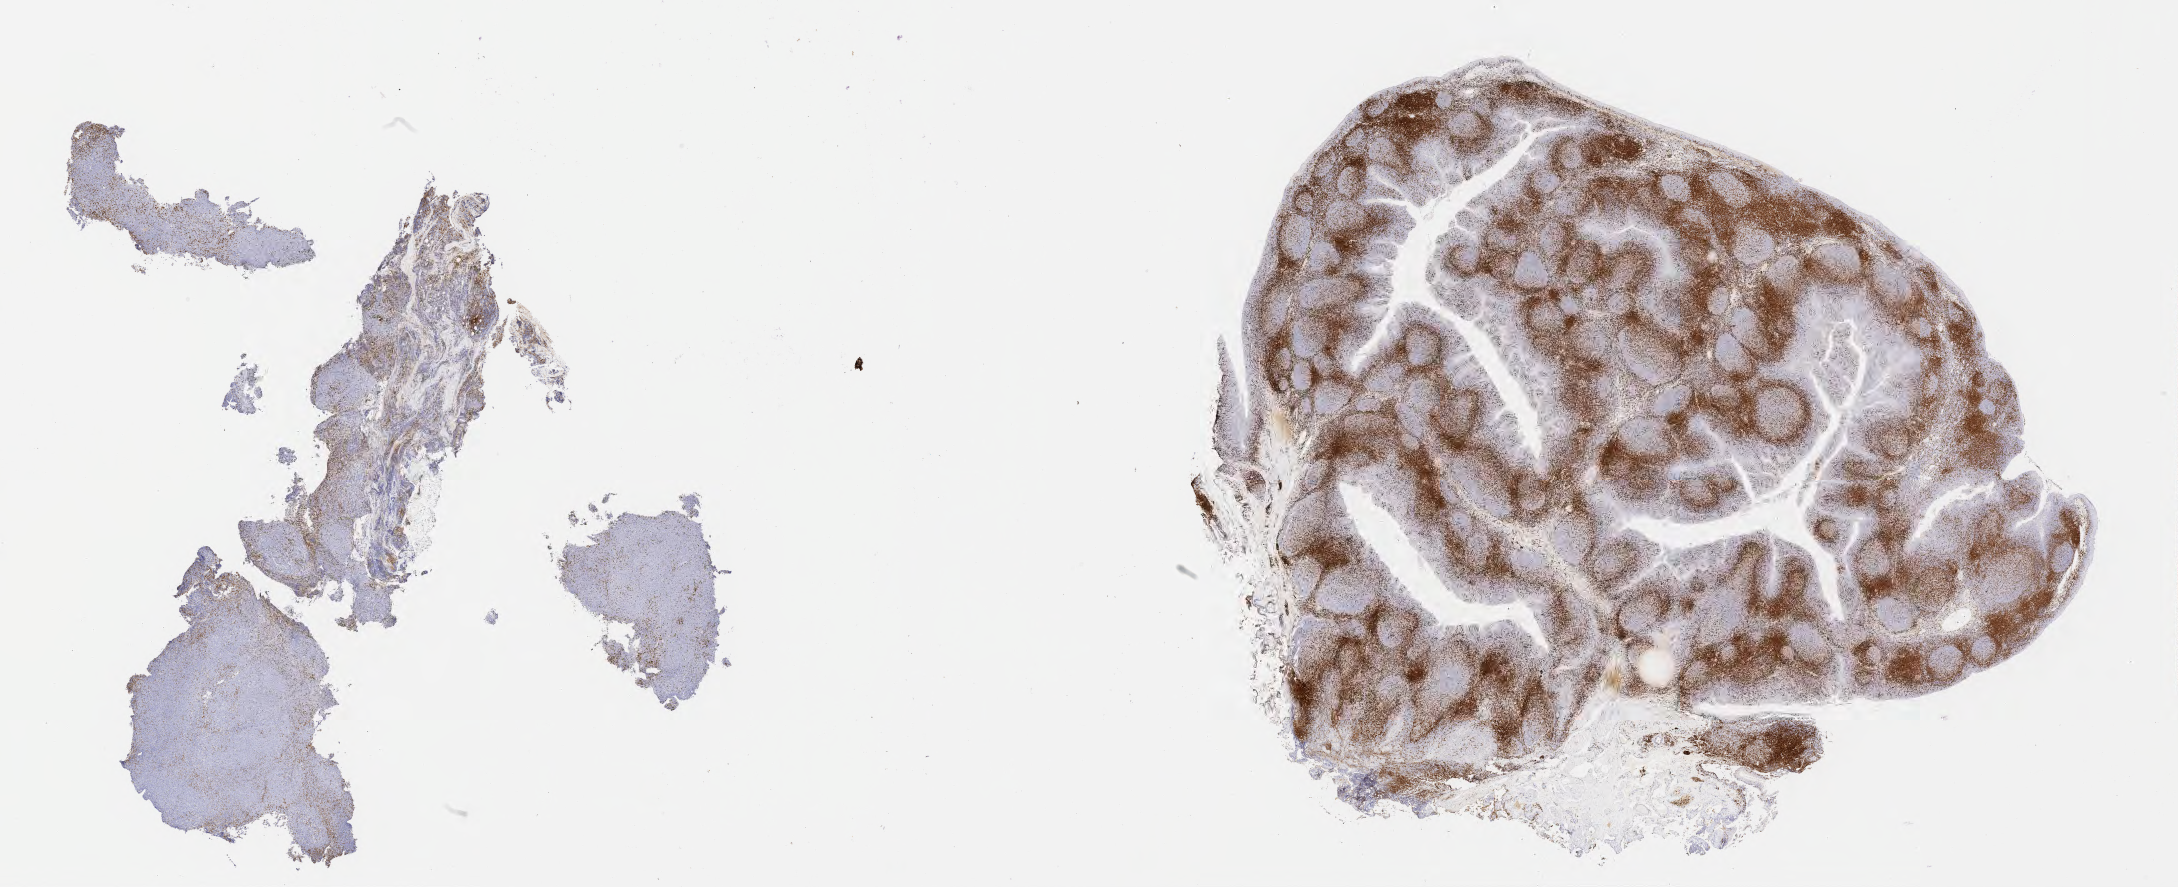
IHC for CD3, whole-slide image — a low-resolution overview of the entire scanned area, about 35.2 x 14.3 mm. Specimen: tumor tissue. Anatomic site: liver. Patient female; aged 36.
• histologic diagnosis: Diffuse large B-cell lymphoma, NOS